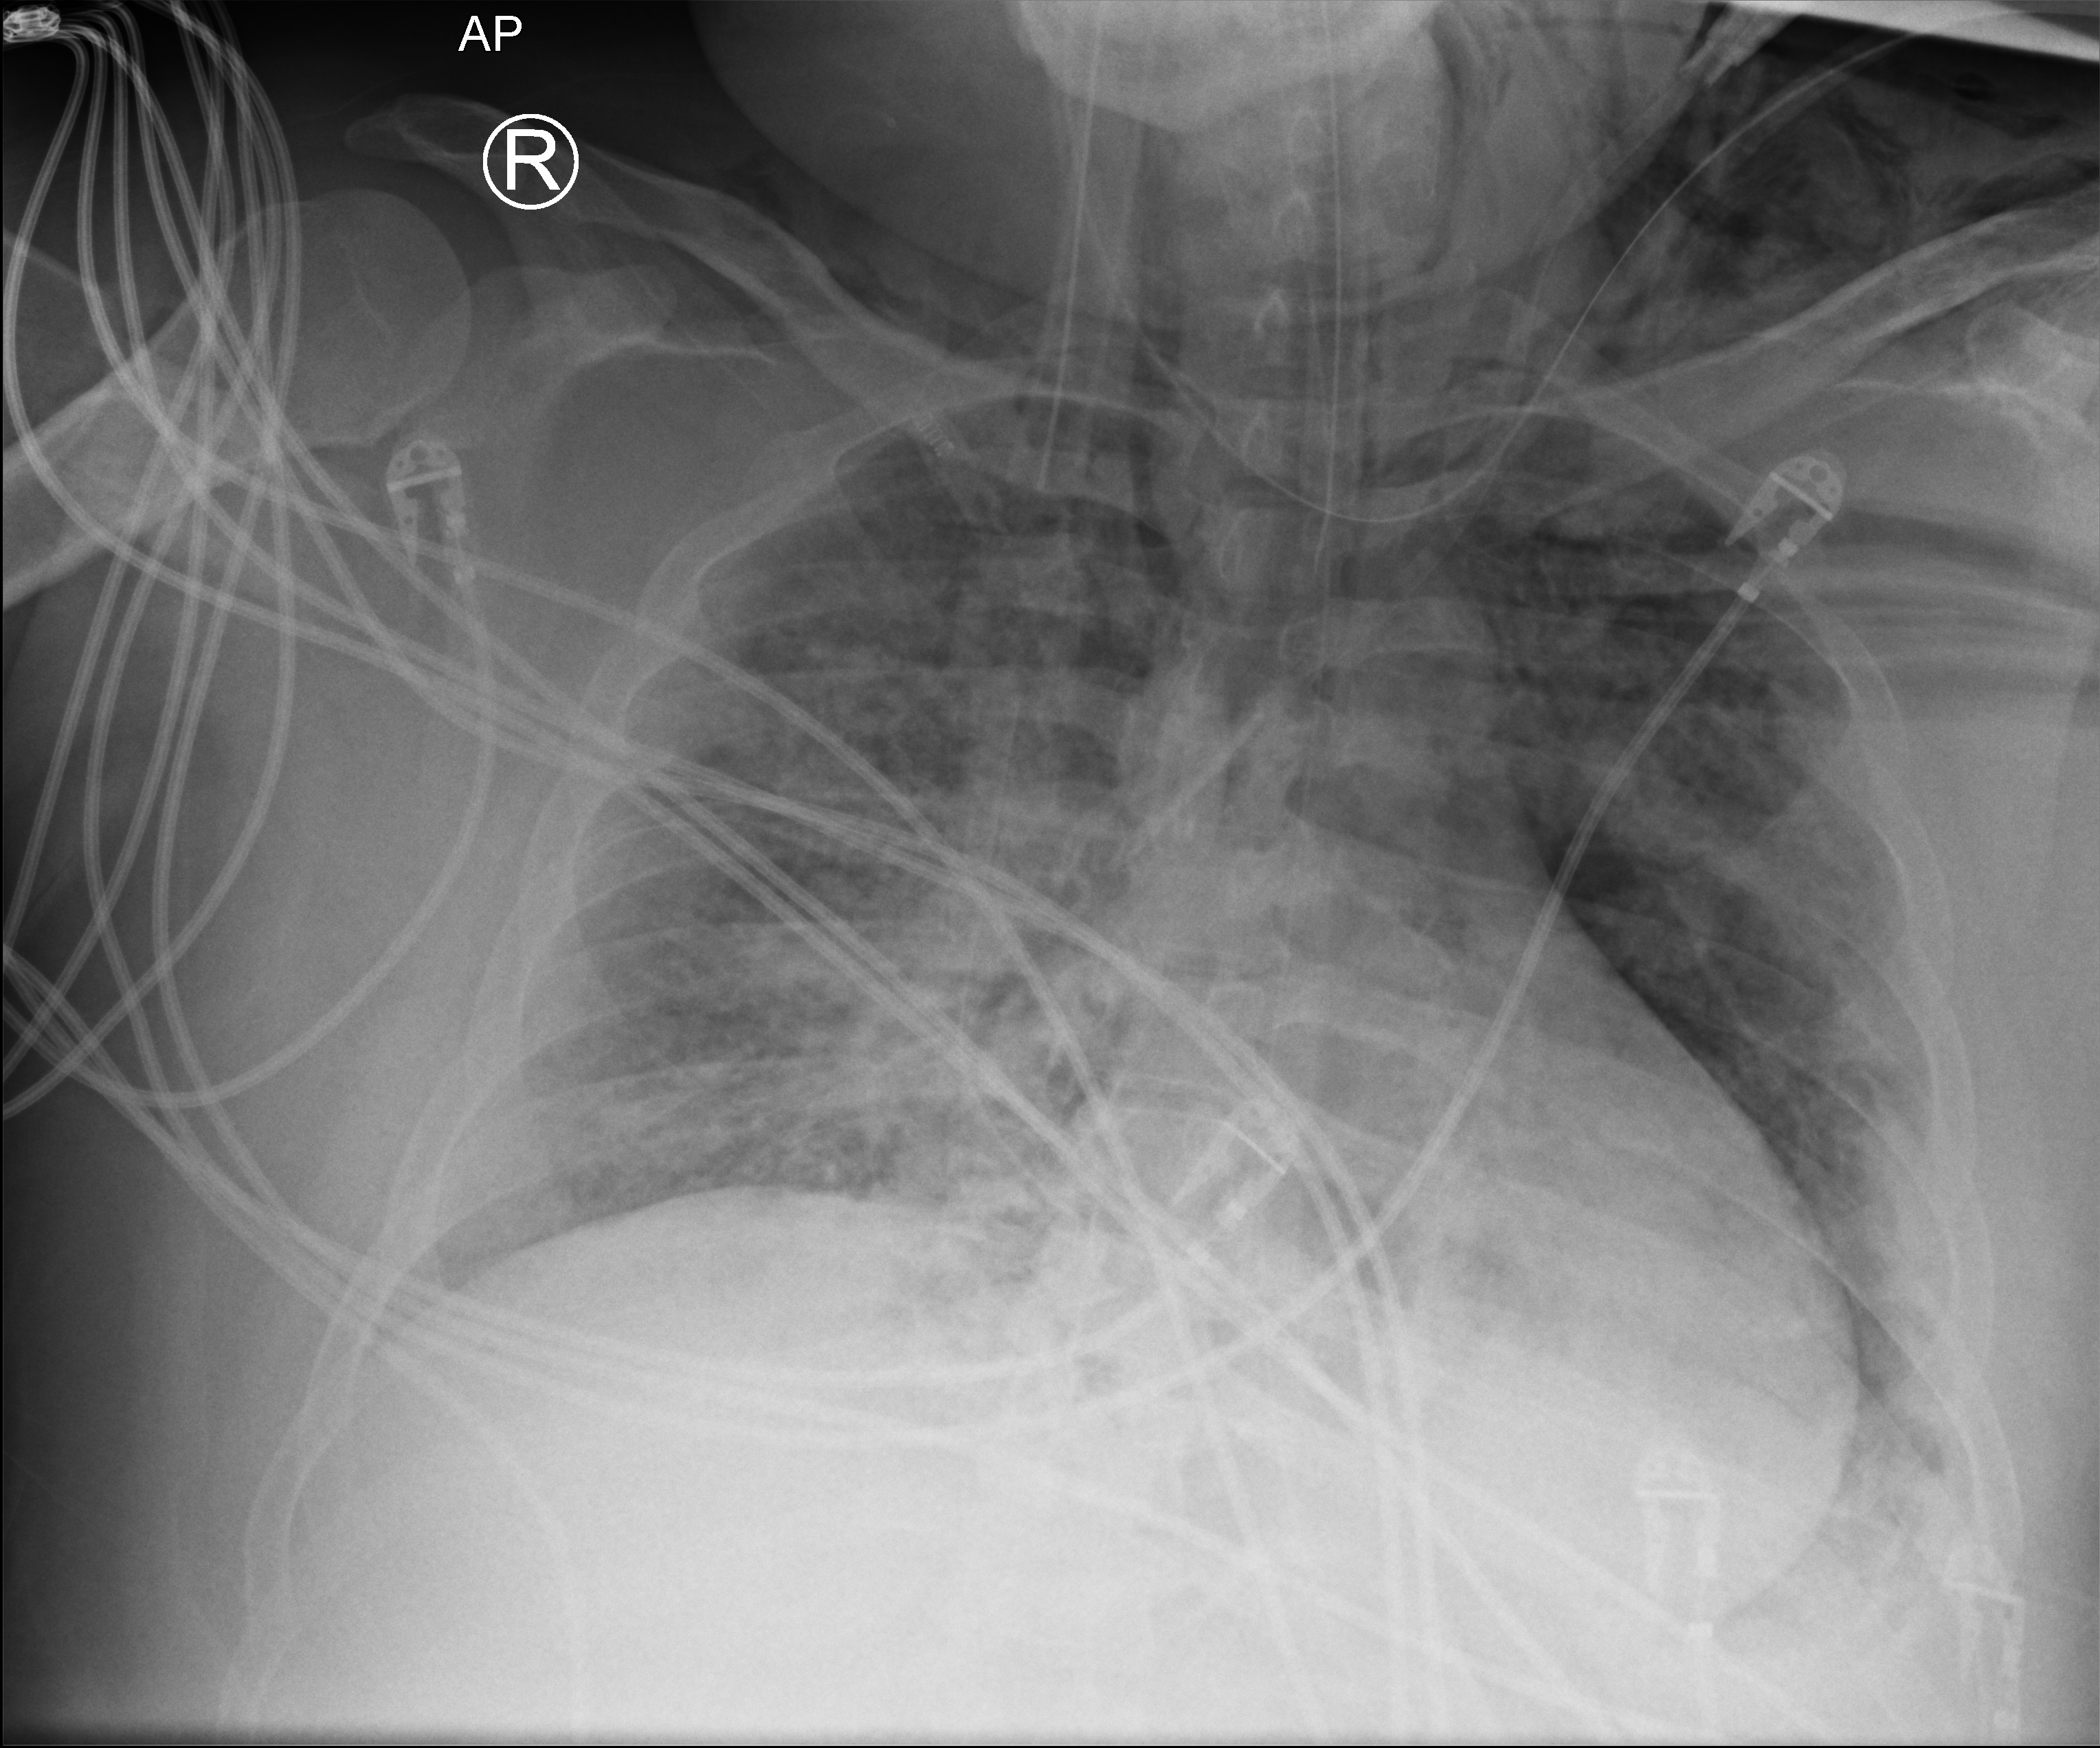
Bedside chest radiograph (computed radiography). Patient hospitalised with COVID-19, aged 18–59 years.
Hospital-stay facts (about this admission, not read from this image; timing relative to this image not recorded): COPD (admission record): no; mechanically ventilated during this hospital stay: yes; admitted to intensive care during this hospital stay: yes.